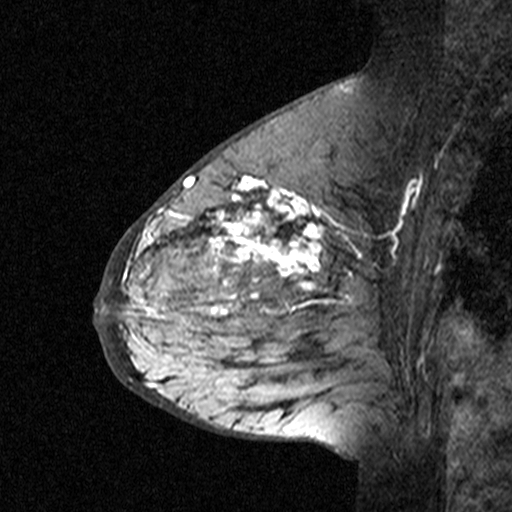
Breast MRI (dynamic contrast-enhanced), one sagittal slice; dynamic contrast-enhanced study with each time point stored as its own series, time point 3 of 4 at this slice position (ordered by acquisition time); 1.5 T; TE 4.5 ms, TR 11 ms; 3 mm slice thickness; 512 × 512 image matrix, field of view 200 × 200 mm. Female patient, age 65 years. From the clinical record (not read from this slice): setting: breast cancer imaged before/during neoadjuvant chemotherapy; receptor status: HER2-positive.
Annotated regions visible in this slice (semi-automatic segmentation, software-assisted and operator-edited):
- analysis volume of interest (the breast-tissue region the enhancement analysis was run in; not a lesion): box from (x=182, y=190) to (x=353, y=361) px
- tumour enhancement mask (voxels above the 90 % enhancement threshold inside the analysis volume of interest): (x=182, y=190)–(x=323, y=315)